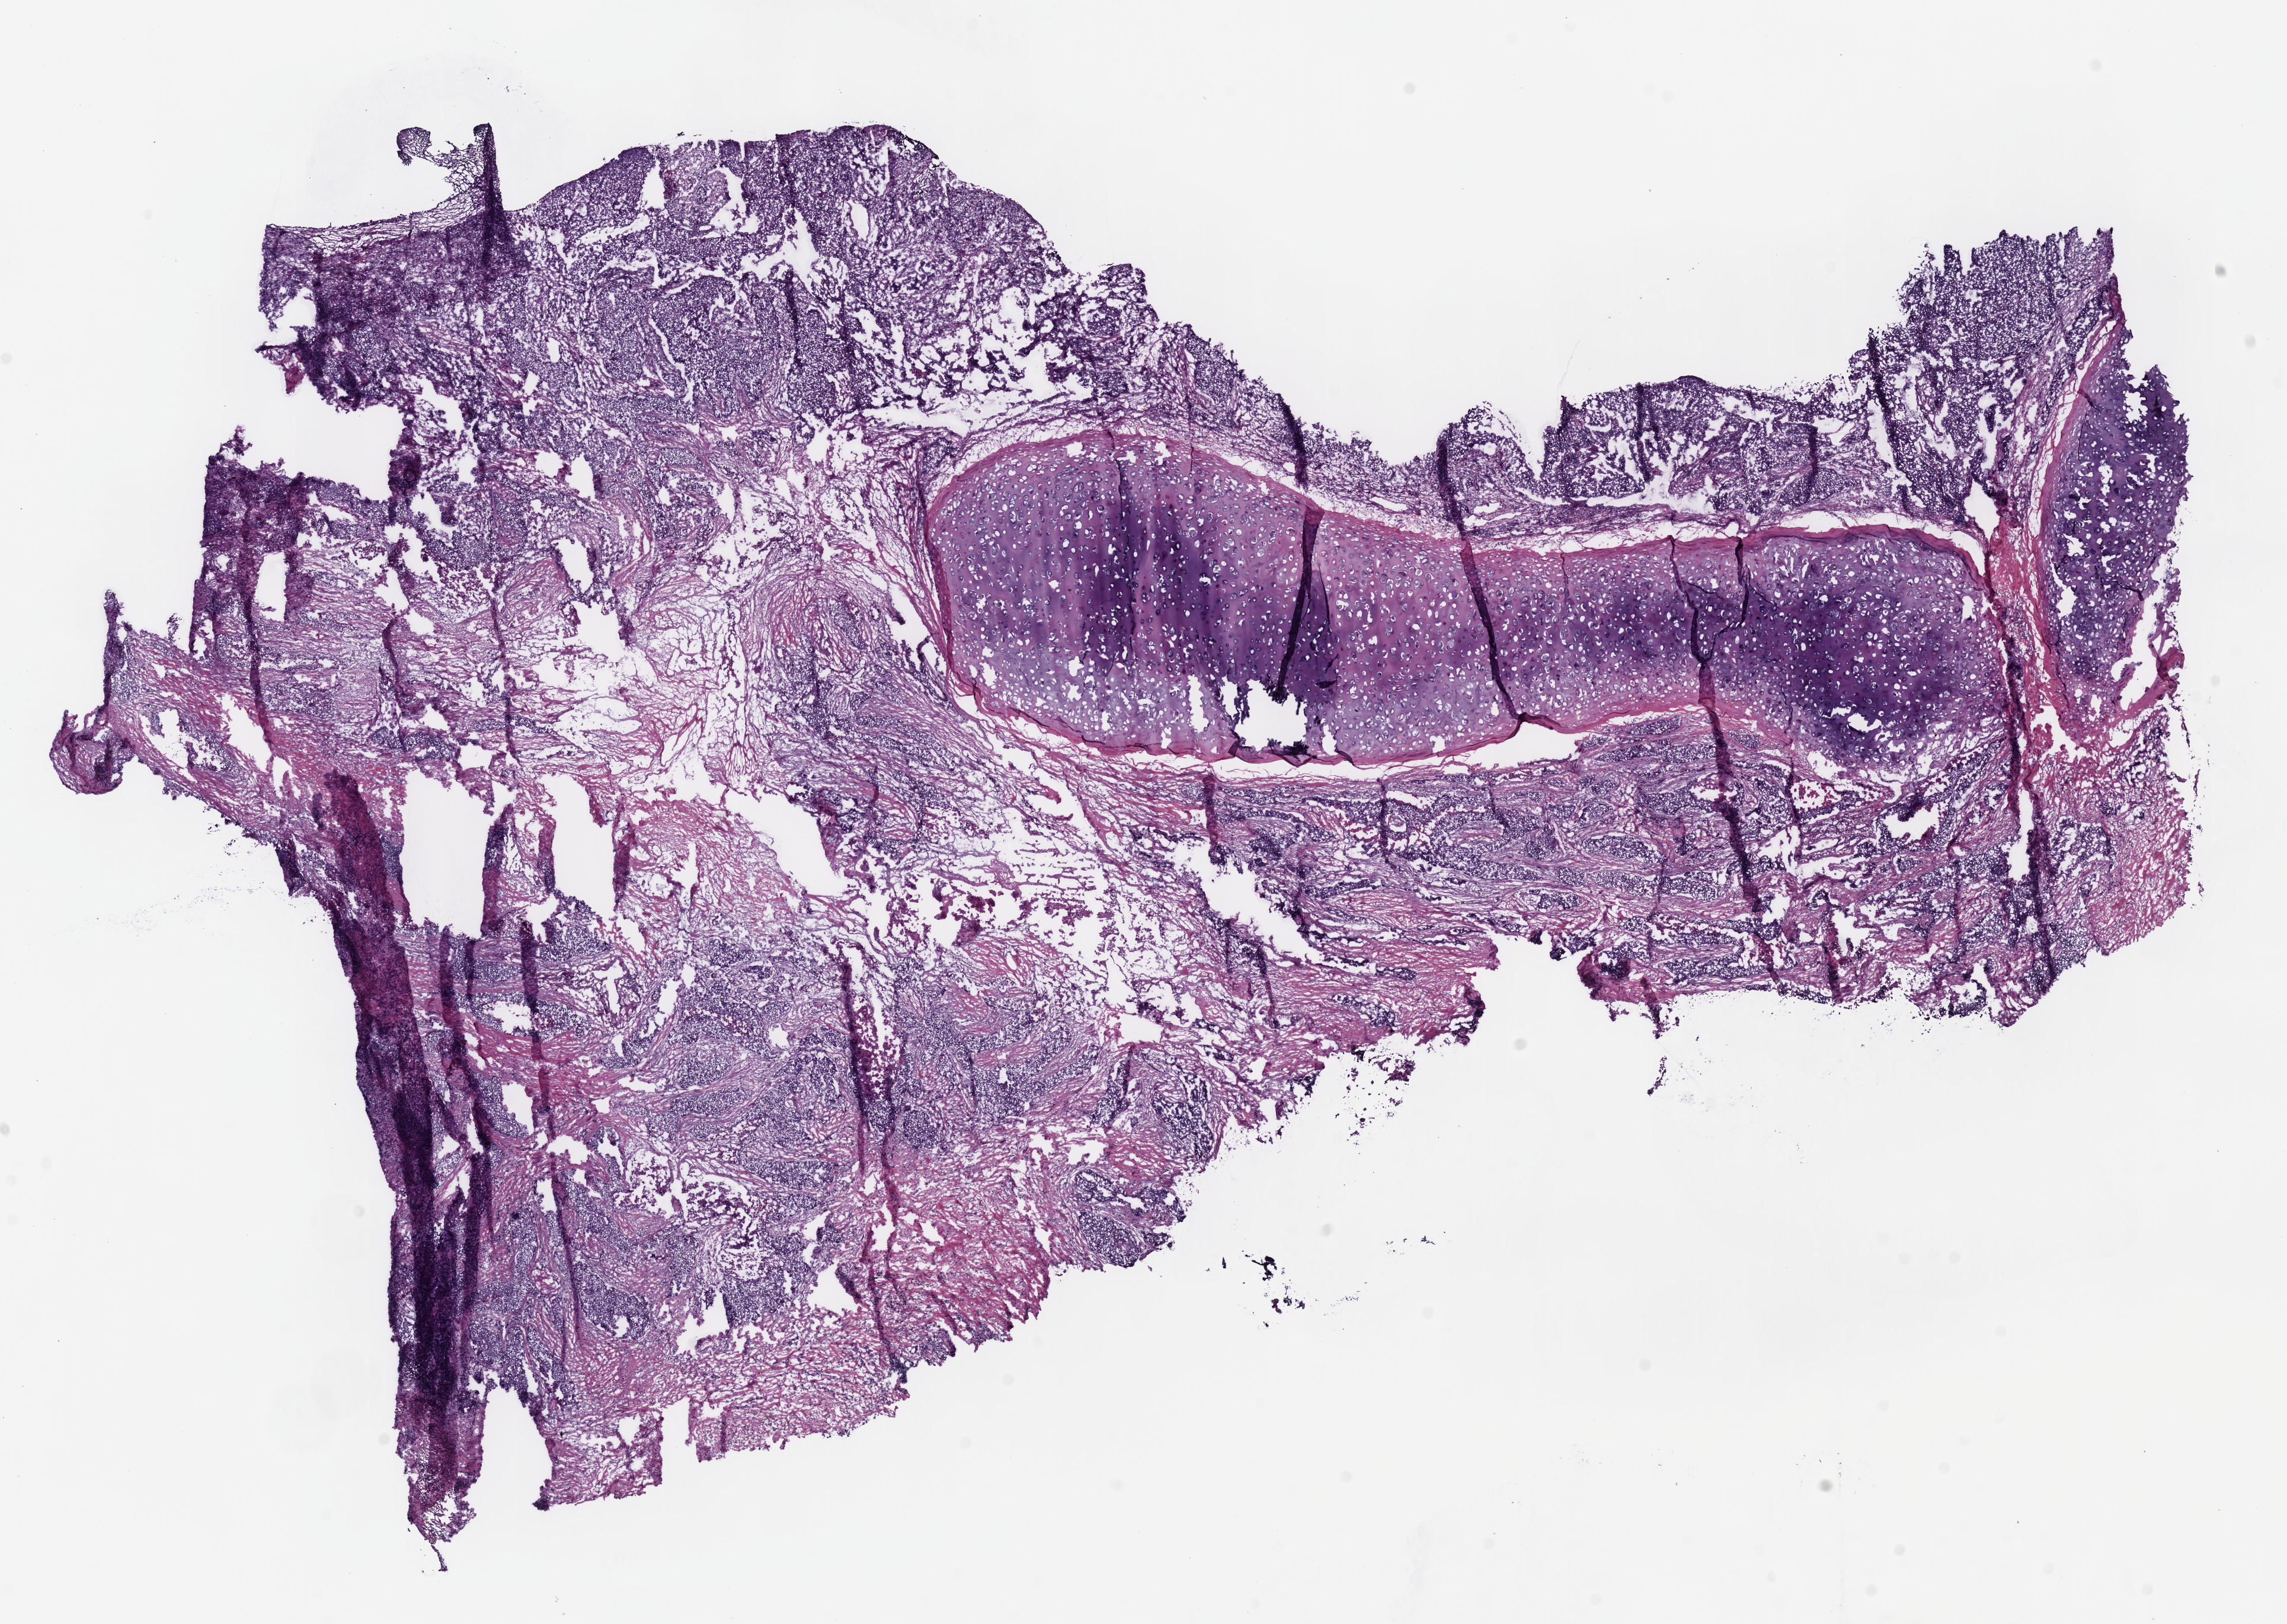
Digitized Hematoxylin and eosin (H&E) stained tissue section (whole slide), whole scanned area (about 15.2 x 10.8 mm, slide scanned at 40x) shown as a low-resolution overview. Frozen section. Sample: primary tumour, lung. Patient: male, age at initial diagnosis 70 years. Composition of this section per pathologist review: tumour cells 70%, tumour nuclei 80%, normal cells 0%, stromal cells 25%, necrosis 5%.
AJCC pathologic stage: IIA (7th edition). Histologic diagnosis: Squamous cell carcinoma, NOS (middle lobe, lung). TNM: T1b N1 M0.